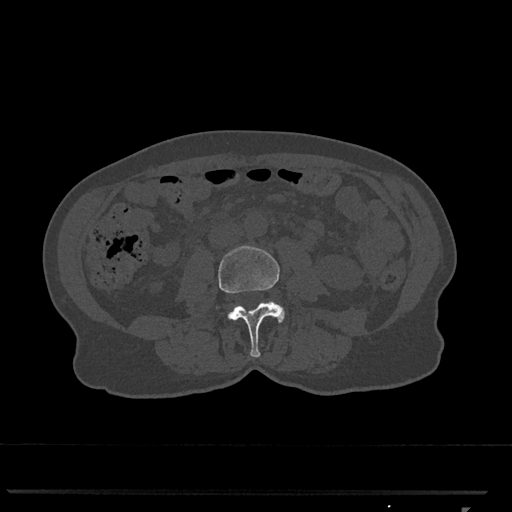
CT including the spine, one axial slice. Slice 263 of 793 in the series (ordered by position). Reconstruction kernel Br40s/3. Bone window (W 1800 / L 400 HU). 0.5 mm slice thickness. 512 × 512 image matrix, field of view 380 × 380 mm. Female patient, age 62 years. Case-level facts recorded for this patient, not image findings: primary cancer: renal.
Structures marked on this image (semi-automatic segmentation, software-assisted and operator-edited):
- L3 vertebra: bounding box <218,246,285,357> (left, top, right, bottom; pixels)